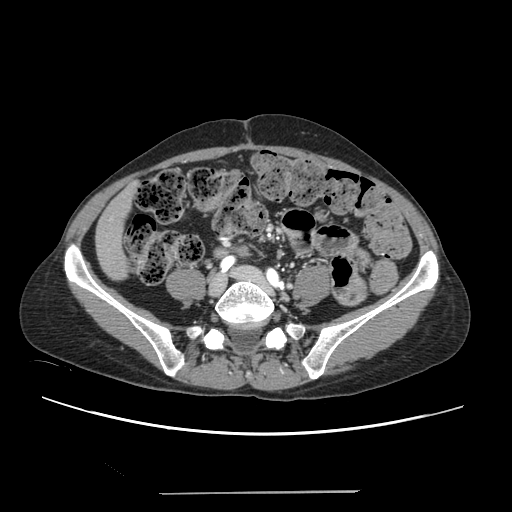
Contrast-enhanced abdominal CT, one axial slice; position 21 of 240 along the scan axis; intravenous contrast given; soft-tissue window (W 400 / L 40 HU); 1.25 mm slice thickness; 512 × 512 image matrix. Female patient, age 60 years. Case-level facts recorded for this patient, not image findings: diagnosis: colorectal cancer liver metastases, imaged before liver resection; multiple liver metastases: no; largest metastasis: 1.5 cm.
Annotated regions visible in this slice (expert manual segmentation):
- liver: box from (x=97, y=187) to (x=134, y=279) px
- planned liver remnant (the part of the liver to remain after resection): (x=97, y=187)–(x=134, y=279)